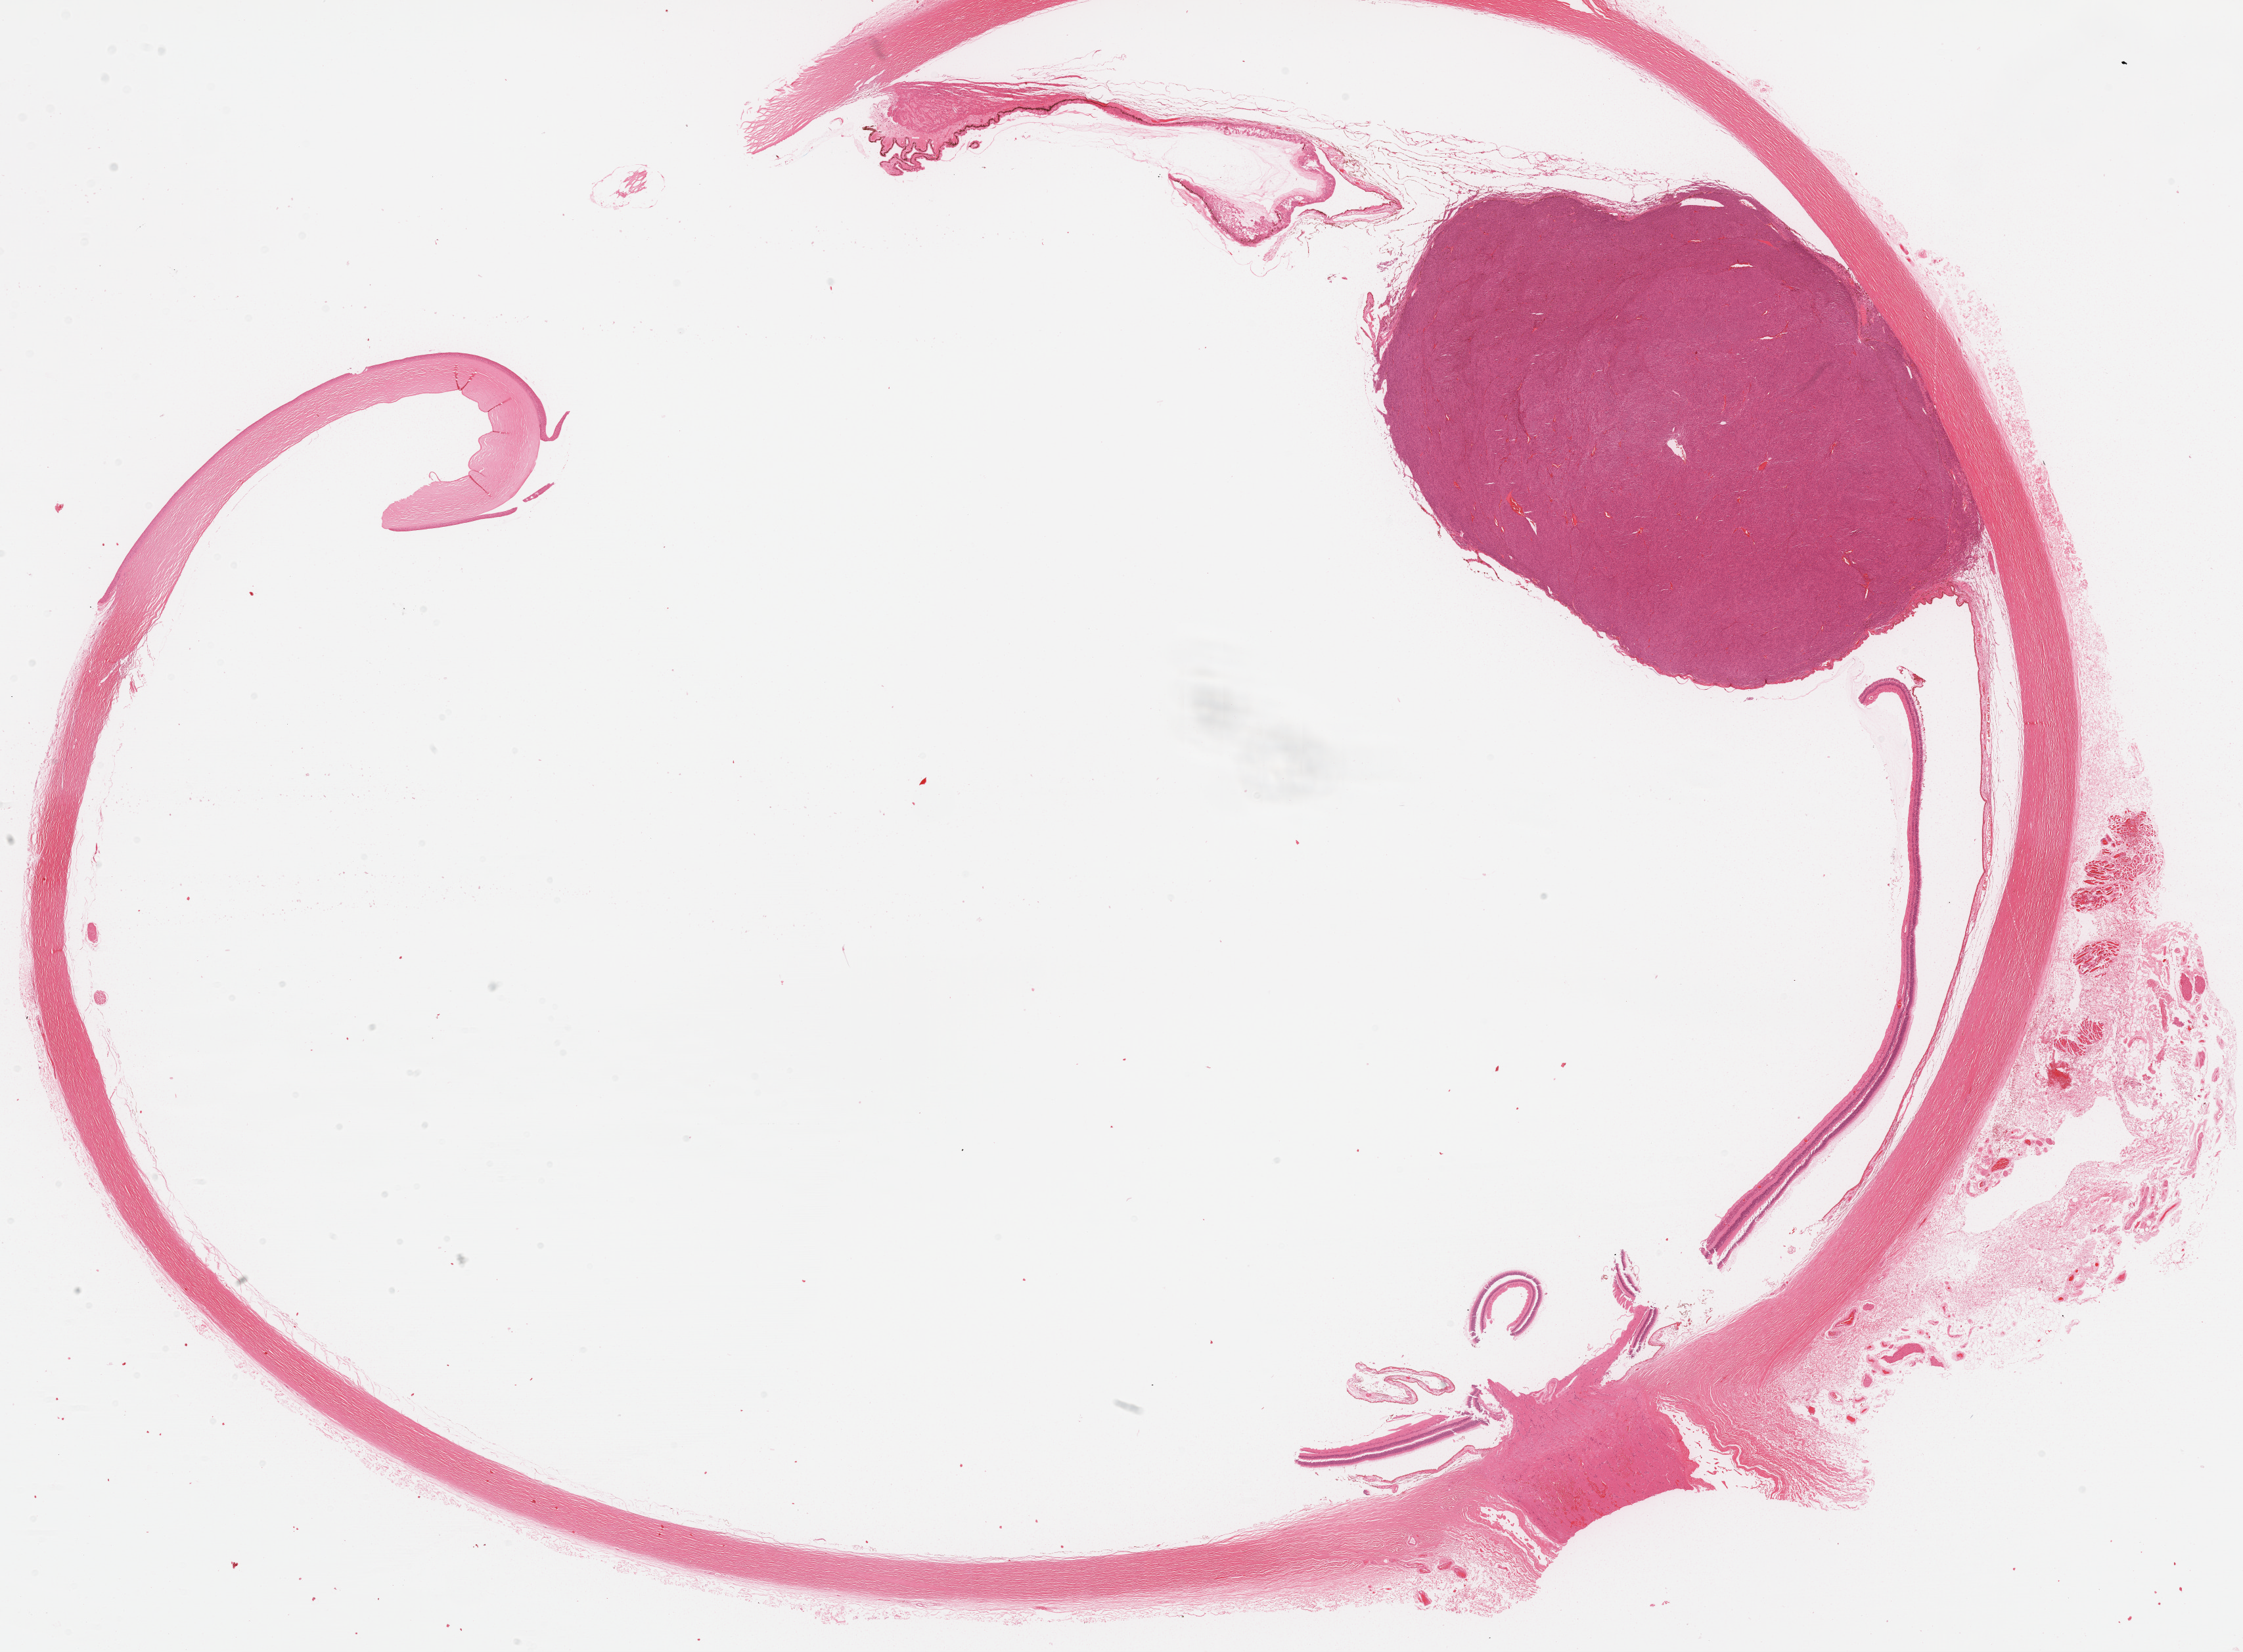
Digitized H&E-stained tissue section (whole slide) — shown as a low-resolution overview of the whole scanned area (about 27.5 x 20.3 mm, from a 20x scan); formalin-fixed paraffin-embedded (FFPE) diagnostic section; primary tumour sample from the uvea. Female, age 71 years at initial diagnosis. Slide review estimates, as recorded: tumour cells 50%, tumour nuclei 60%, normal cells 50%, stromal cells 0%, necrosis 0%. Inflammatory infiltration, as recorded: lymphocyte infiltration 1%, monocyte infiltration 0%, neutrophil infiltration 0%.
Pathologic diagnosis: Spindle cell melanoma, type B (choroid). AJCC pathologic stage: IIA.